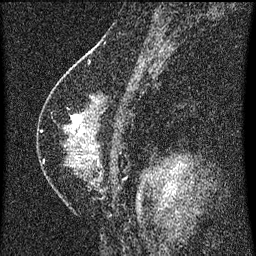
Breast MRI (dynamic contrast-enhanced), one sagittal slice. Position 39 of 60 along the scan axis. Dynamic contrast-enhanced series, image 2 of 3 at this slice position (ordered by acquisition). 1.5 T. TE 4.2 ms, TR 8 ms. 2 mm slice thickness. 256 × 256 image matrix, field of view 180 × 180 mm. Patient: female, 47 years.
Outlined on this slice (semi-automatically segmented with operator editing):
- analysis volume of interest (the breast-tissue region the enhancement analysis was run in; not a lesion): bounding box (x1, y1, x2, y2) in pixels: (42, 92, 129, 199)
- tumour enhancement mask (voxels above the 70 % enhancement threshold inside the analysis volume of interest): (71, 116, 81, 131)